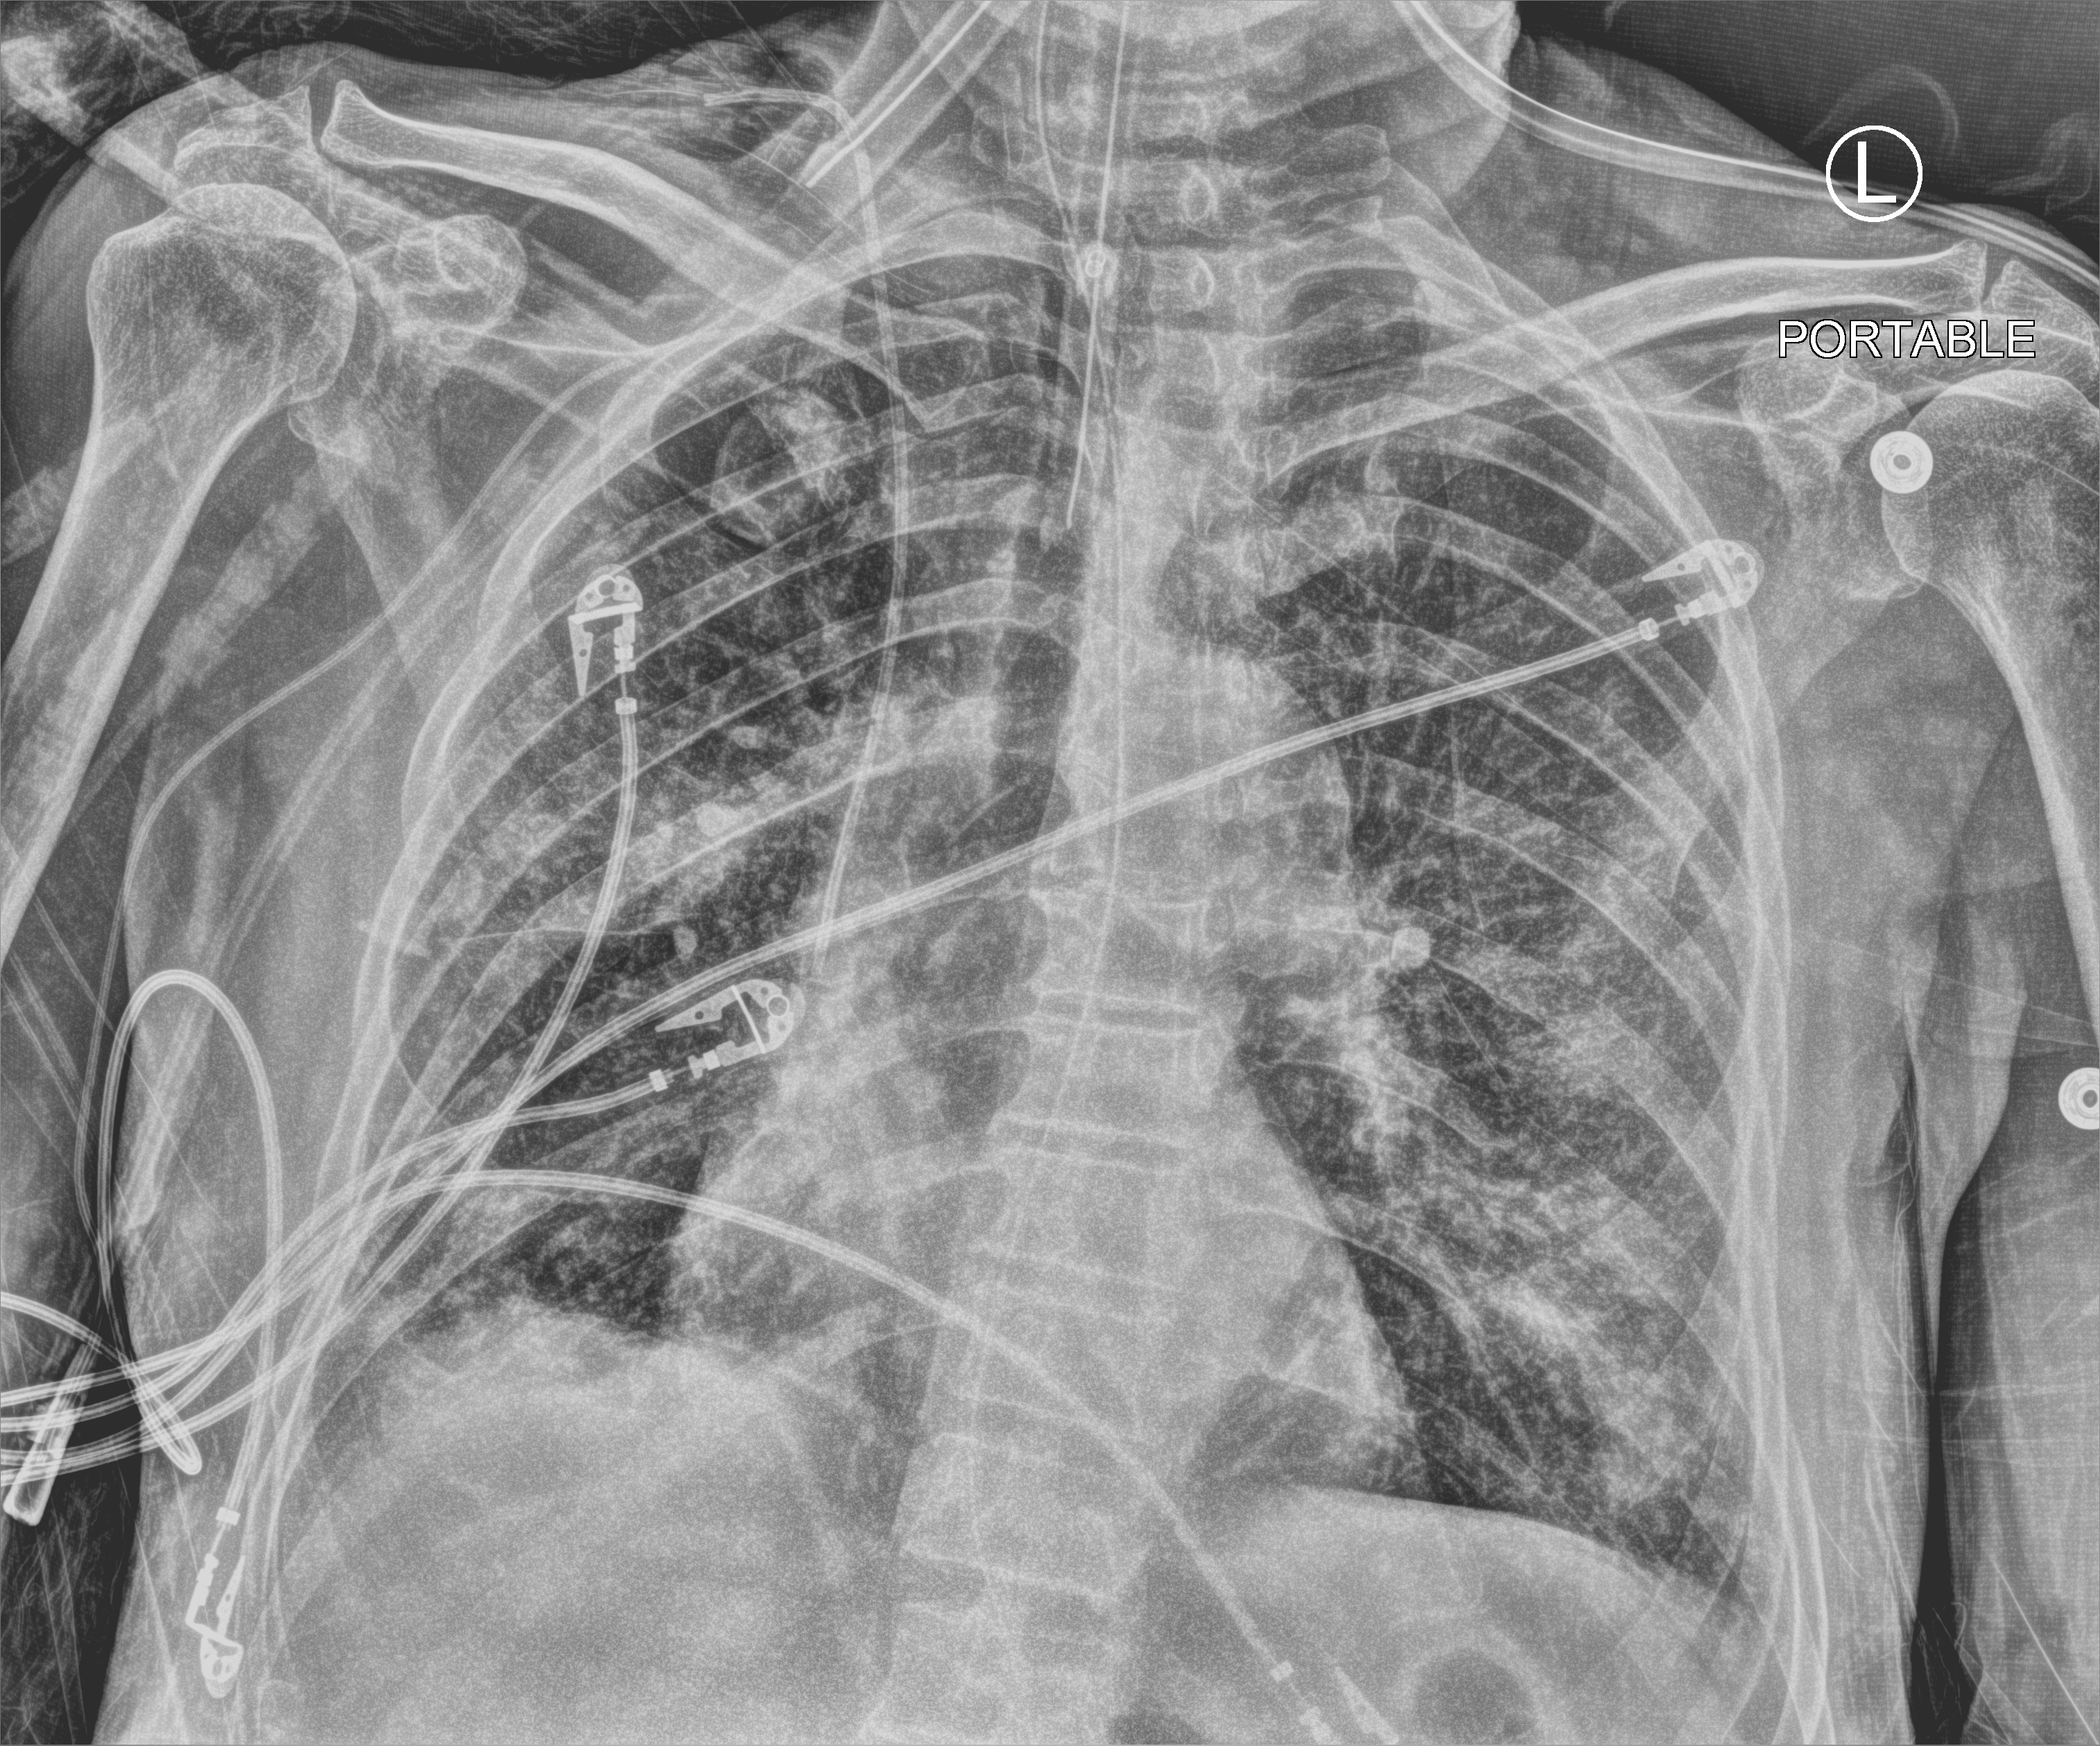
Portable chest radiograph; anteroposterior (AP) projection. Patient hospitalised with COVID-19; male, aged 75–90 years.
Hospital-stay facts (about this admission, not read from this image; timing relative to this image not recorded): chronic kidney disease (admission record): no; smoking status (admission record): never.